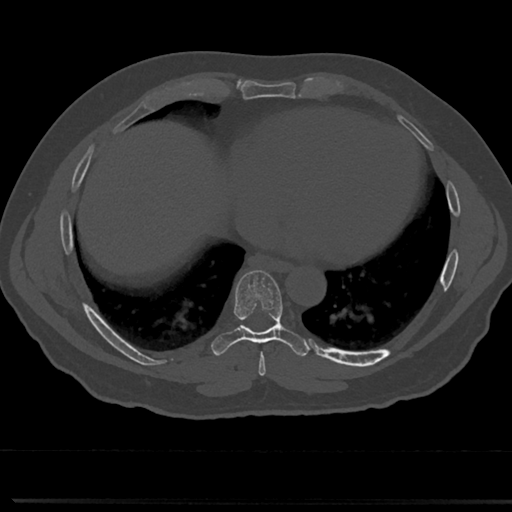
CT including the spine, one axial slice. Slice 359 of 817 in the series (ordered by position). Reconstruction kernel Br40s/3. Bone window (W 1800 / L 400 HU). 0.5 mm slice thickness. 512 × 512 image matrix, field of view 355 × 355 mm. Patient: male, 61 years. Case-level facts recorded for this patient, not image findings: primary cancer: prostate.
Outlined on this slice (semi-automatic segmentation, software-assisted and operator-edited):
- T7 vertebra: bounding box (x1, y1, x2, y2) in pixels: (239, 329, 284, 362)
- T8 vertebra: (237, 270, 283, 336)